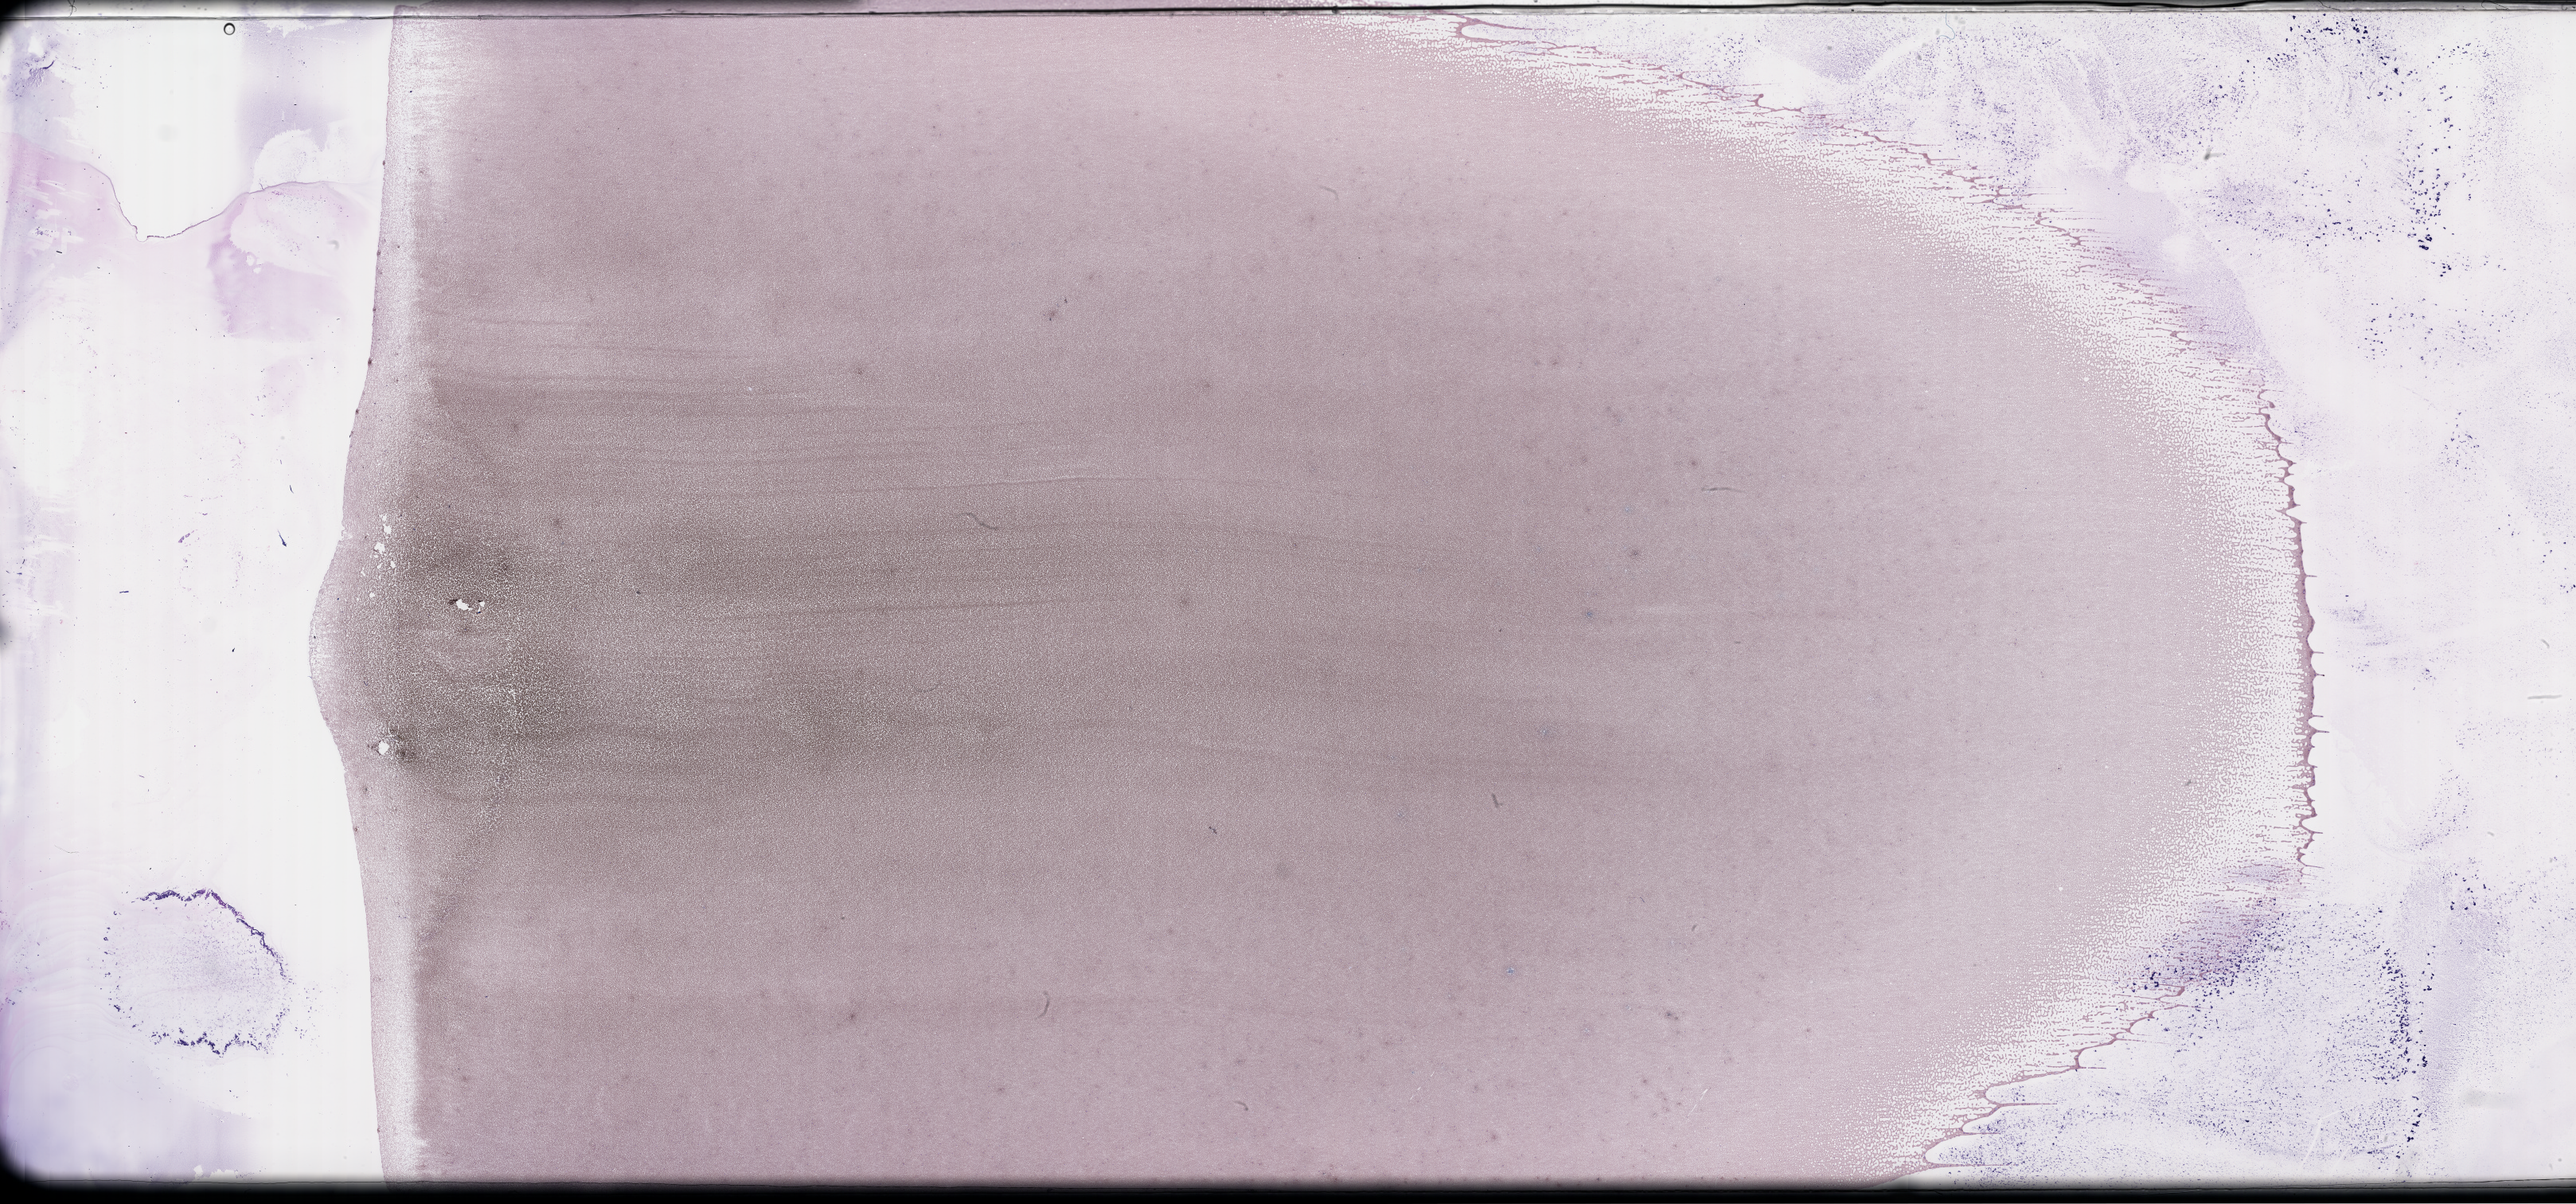
Wright–Giemsa-stained whole blood smear, whole-slide image — a low-resolution overview of the entire scanned area, about 52.3 x 24.4 mm, smear from an EDTA sample, specimen time point: collected on treatment. Patient sex: male.
Patient diagnosis: Plasma Cell Myeloma.